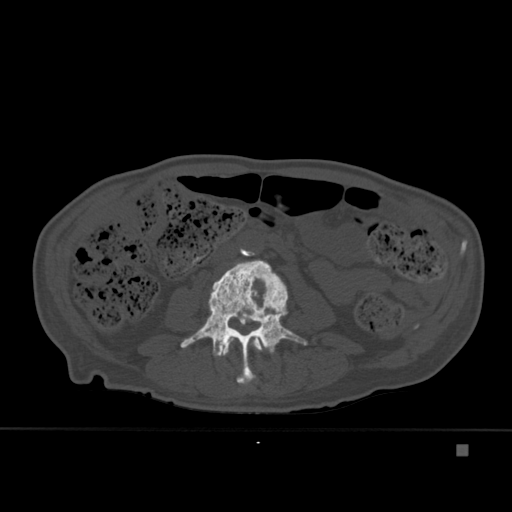
CT including the spine, one axial slice. Position 144 of 451 along the scan axis. Bone window (W 1800 / L 400 HU). 512 × 512 image matrix. Male patient, age 75 years. Case-level facts recorded for this patient, not image findings: primary cancer: prostate.
Annotated regions visible in this slice (semi-automatically segmented with operator editing):
- L2 vertebra: bounding box [x1, y1, x2, y2] px = [221, 336, 263, 385]
- L3 vertebra: [180, 259, 307, 383]